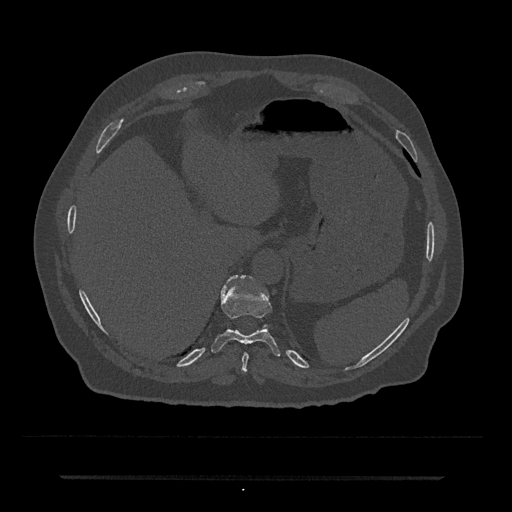
CT including the spine, one axial slice; slice 229 of 797 in the series (ordered by position); 120 kVp; bone window (W 1800 / L 400 HU); 0.5 mm slice thickness; 512 × 512 image matrix, field of view 437 × 437 mm. Patient: male, 69 years. From the clinical record (not read from this slice): primary cancer: prostate.
Outlined on this slice (semi-automatically segmented with operator editing):
- T10 vertebra: bounding box (x1, y1, x2, y2) in pixels: (211, 275, 281, 357)
- T11 vertebra: (228, 275, 245, 282)
- T9 vertebra: (242, 352, 249, 373)